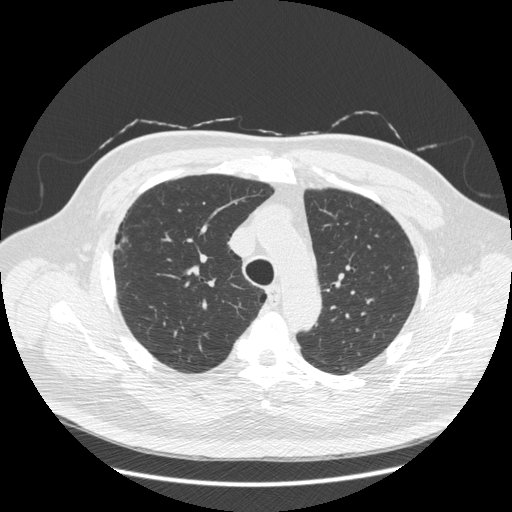
Low-dose screening chest CT, axial slice. Second annual screen. Lung window (W 1500 / L -600 HU). 1.25 mm slice thickness. Slice 69 of 281 in the series. 512 × 512 image matrix. Male participant, aged 66 years at enrolment. Current smoker at enrolment.
Expert-annotated lung lesion, bounding box <102,214,141,268> (left, top, right, bottom; pixels). The screening reader recorded 2 non-calcified nodules or masses ≥4 mm on this exam; which of them this box marks is not recorded. Official screen result: positive, other. Lung cancer was diagnosed 403 days after this screen: non-small cell carcinoma, right upper lobe, stage IV (AJCC 6th edition), 50 mm at pathology.